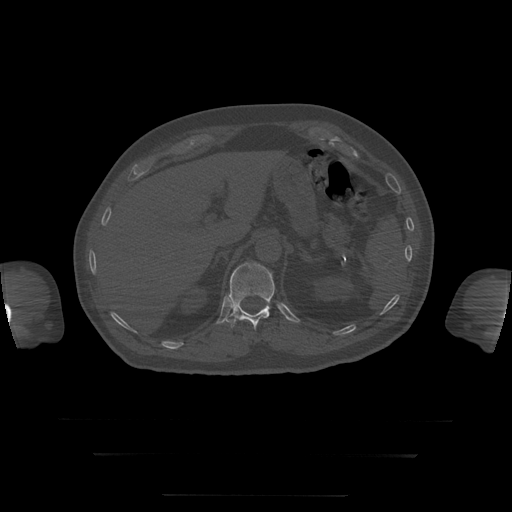
CT including the spine, one axial slice; slice 75 of 397 in the series (ordered by position); bone window (W 1800 / L 400 HU); 1.25 mm slice thickness; 512 × 512 image matrix, field of view 510 × 510 mm. Patient age 73 years. Case-level facts recorded for this patient, not image findings: primary cancer: prostate.
Outlined on this slice (semi-automatically segmented with operator editing):
- T12 vertebra: box from (x=228, y=263) to (x=275, y=330) px